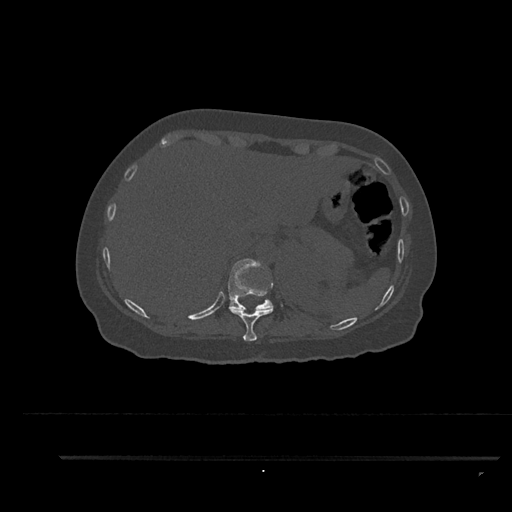
CT including the spine, one axial slice; position 341 of 797 along the scan axis; reconstruction kernel Br40s/3; 120 kVp; bone window (W 1800 / L 400 HU); 0.5 mm slice thickness; 512 × 512 image matrix, field of view 408 × 408 mm. Female patient, age 44 years. From the clinical record (not read from this slice): primary cancer: renal; vertebrae with lytic lesions (as recorded): L1.
Annotated regions visible in this slice (semi-automatically segmented with operator editing):
- T10 vertebra: bounding box <228,307,273,341> (left, top, right, bottom; pixels)
- T11 vertebra: <228,259,274,311>